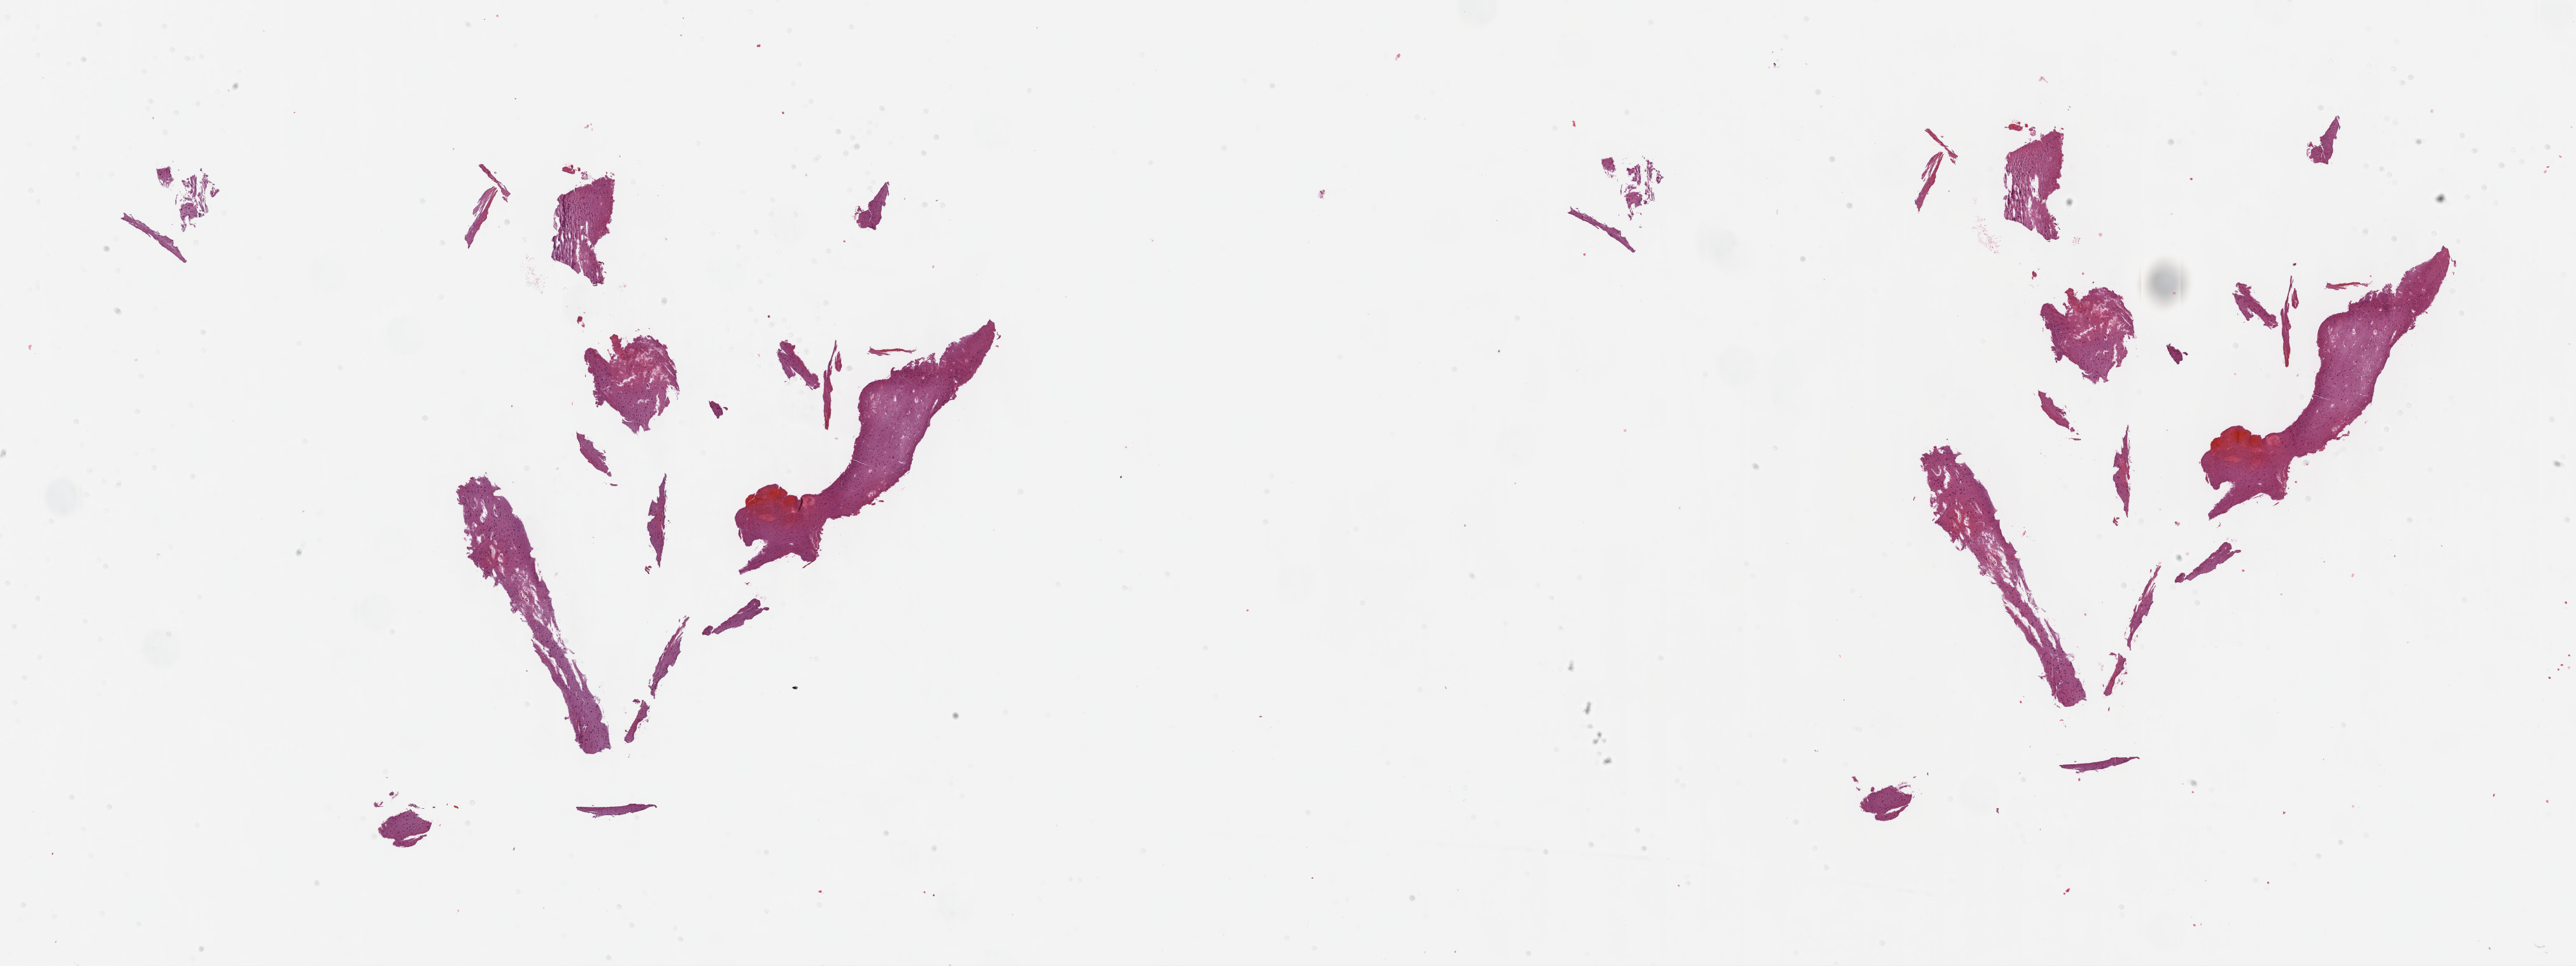
Digitized H&E-stained tissue section (whole slide) — shown as a low-resolution overview of the whole scanned area (about 32.7 x 12.3 mm, from a 40x scan), formalin-fixed paraffin-embedded (FFPE) diagnostic section, sample: primary tumour, brain. Patient: female, age at initial diagnosis 18 years. Histologic grade: G2 (moderately differentiated).
Pathologic diagnosis: Mixed glioma.